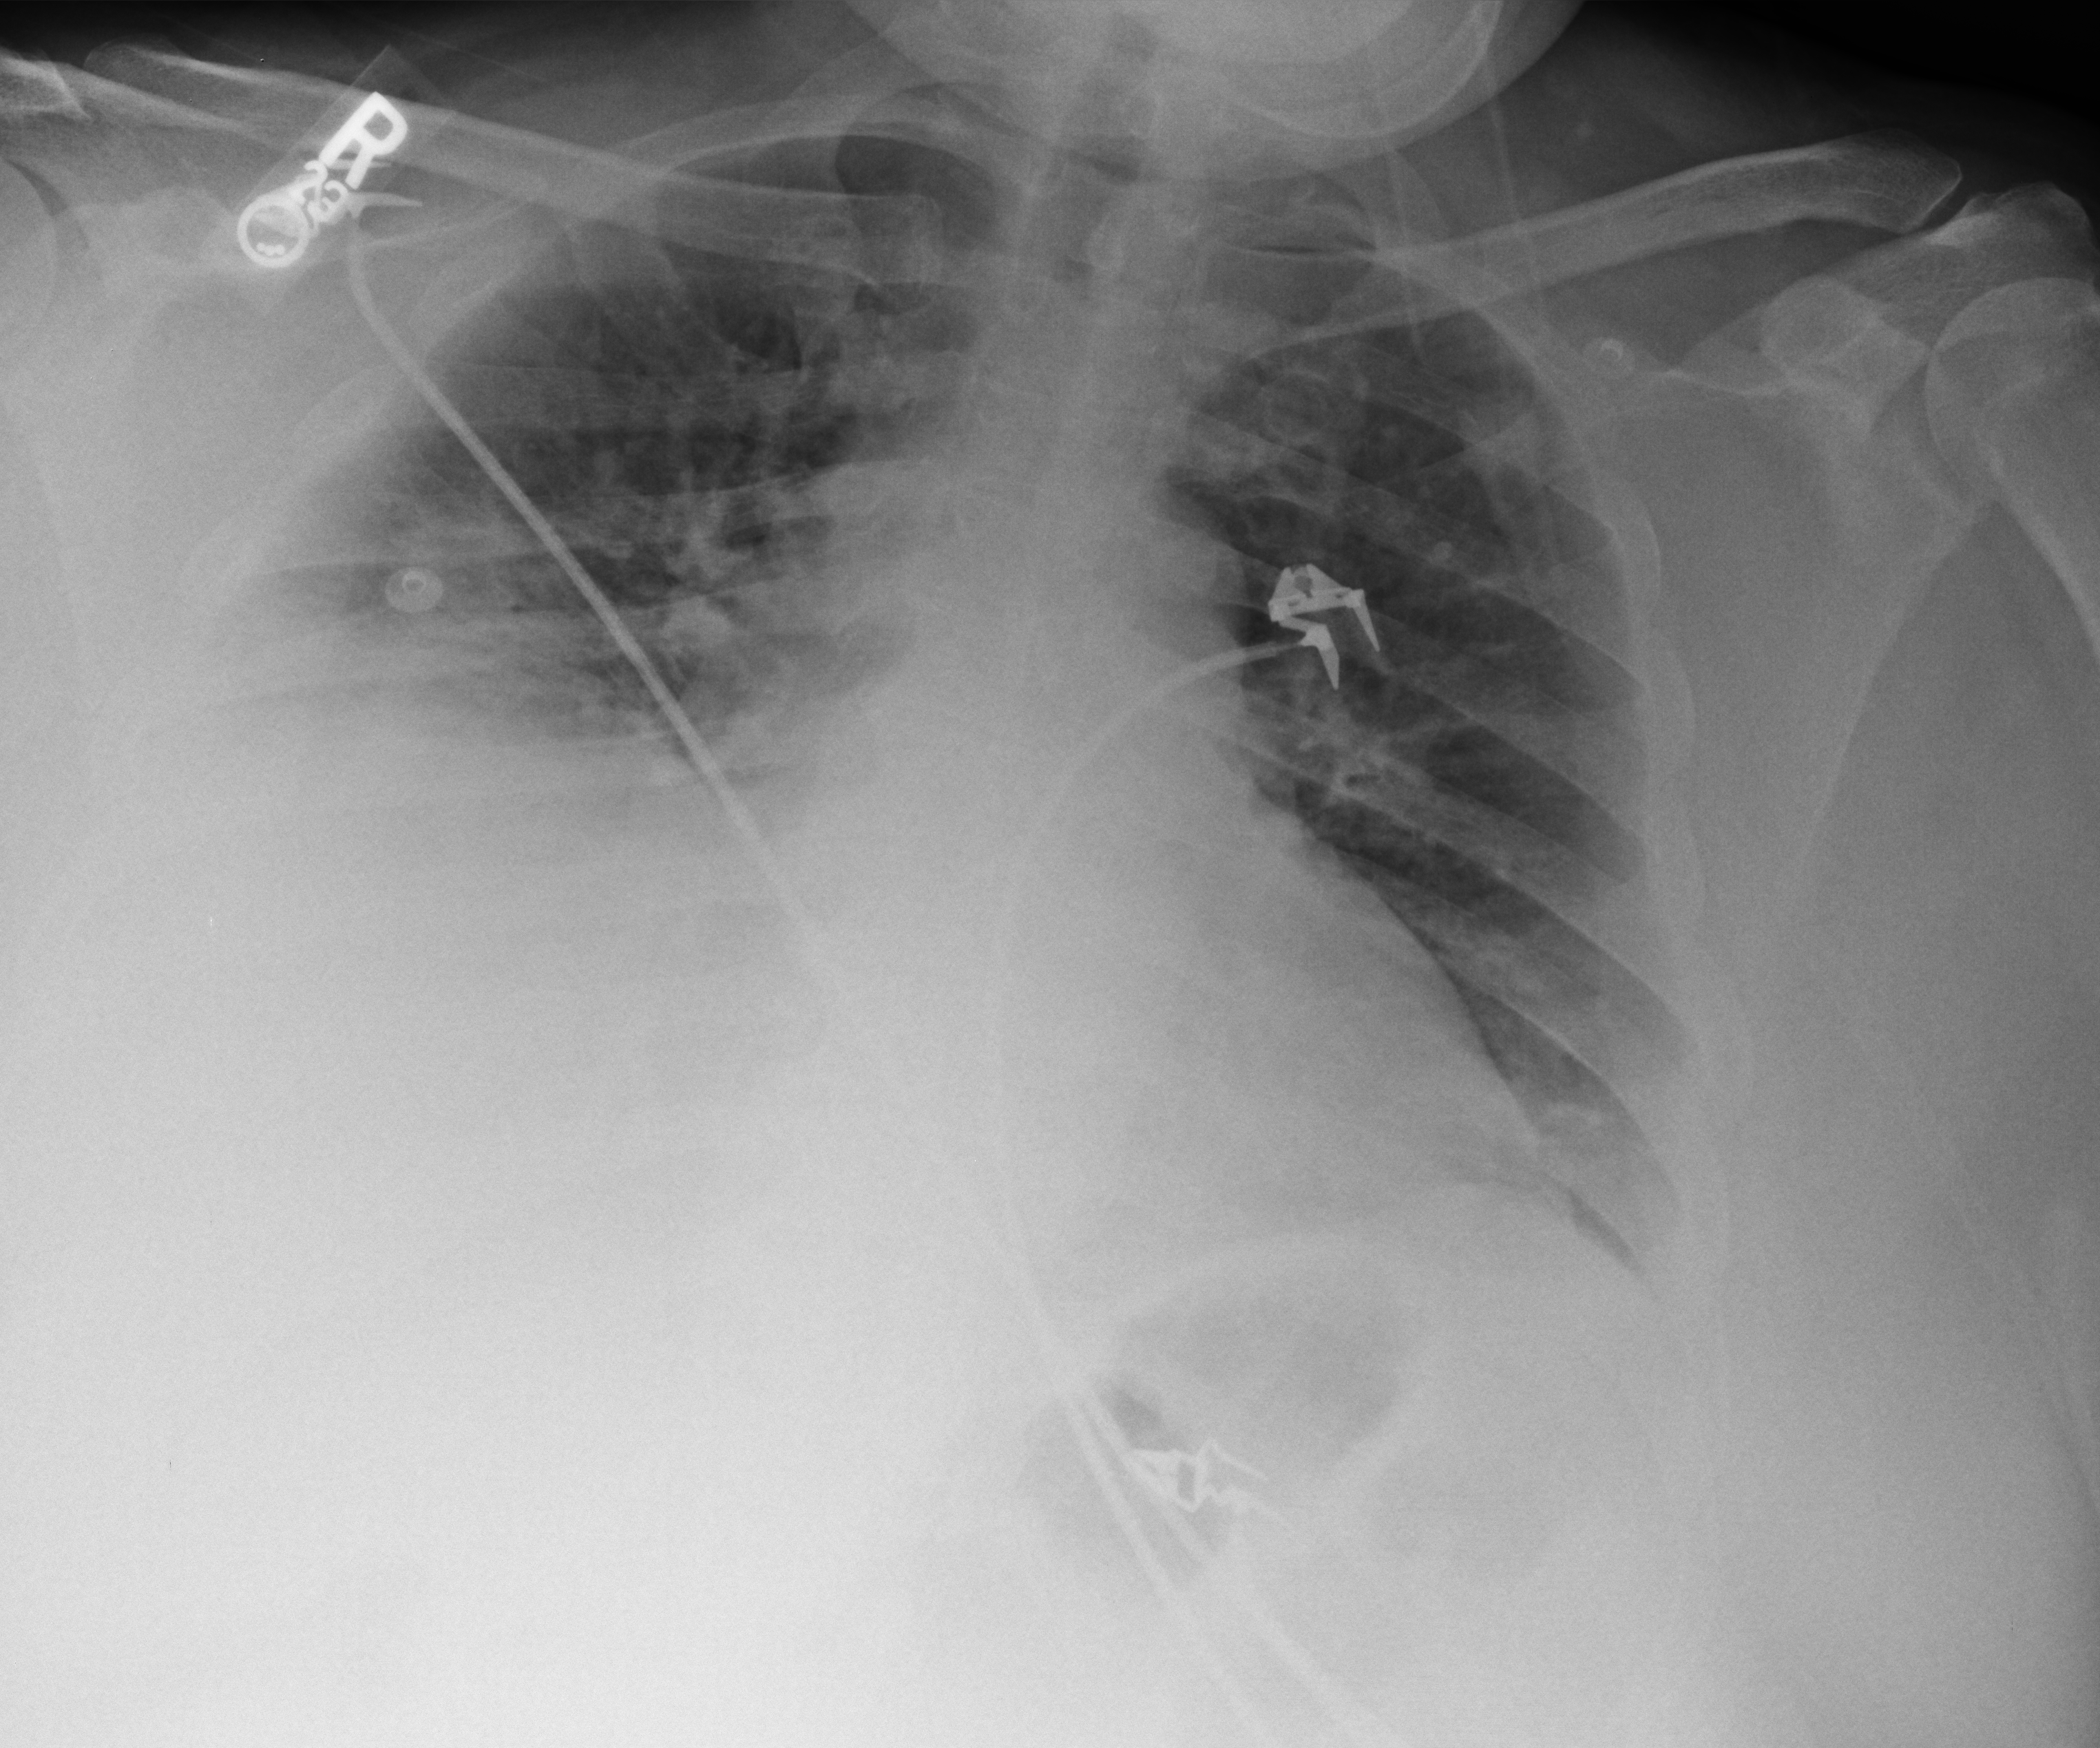
Chest X-ray (portable); anteroposterior (AP) projection. Patient hospitalised with COVID-19; male, aged 18–59 years.
Hospital-stay facts (about this admission, not read from this image; timing relative to this image not recorded):
- diabetes (admission record): yes
- admitted to intensive care during this hospital stay: no